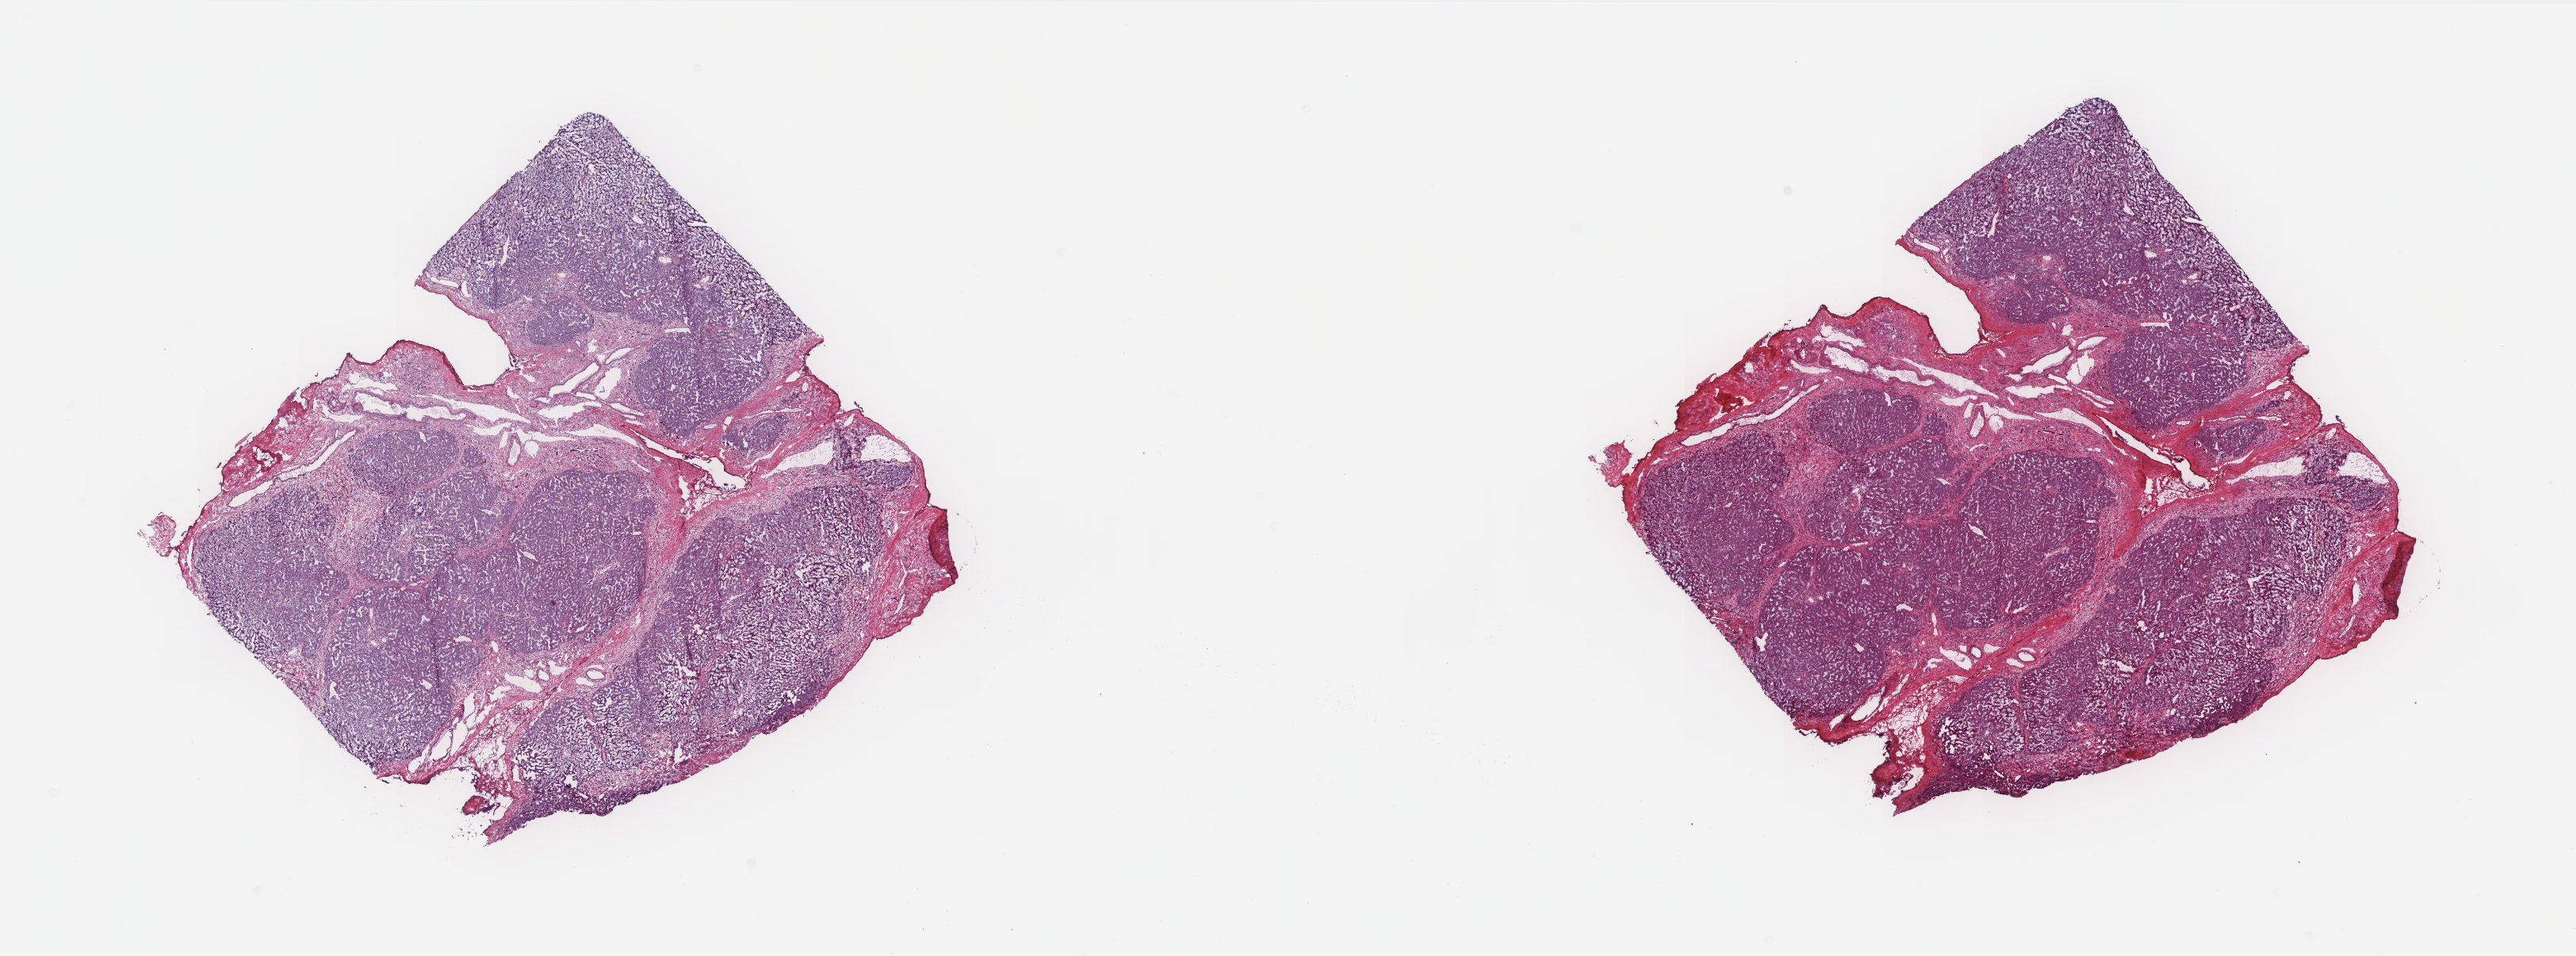
Digitized H&E tissue section (whole slide) — low-resolution overview of the scanned area, about 25.9 x 9.6 mm (slide scanned at 20x); frozen section from the top of the tissue portion; liver, solid tissue normal (non-tumour tissue) sample. Male patient; age at initial diagnosis 65 years. Pathologist review of this section (percent, as recorded): tumour cells 0%, tumour nuclei 0%, normal cells 80%, stromal cells 20%, necrosis 0%. Inflammatory infiltration, as recorded: lymphocyte infiltration 2%, monocyte infiltration 0%, neutrophil infiltration 0%.
This section: solid tissue normal (non-tumour) sample from the same patient. Patient diagnosis: Hepatocellular carcinoma, NOS.